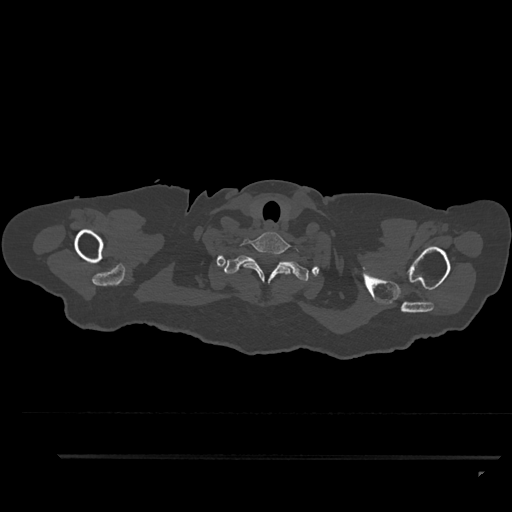
CT including the spine, one axial slice; slice 781 of 797 in the series (ordered by position); bone window (W 1800 / L 400 HU); 0.5 mm slice thickness; 512 × 512 image matrix, field of view 408 × 408 mm. Patient: female, 44 years. Case-level facts recorded for this patient, not image findings: primary cancer: renal.
Structures marked on this image (semi-automatically segmented with operator editing):
- T1 vertebra: bounding box <224,255,309,281> (left, top, right, bottom; pixels)